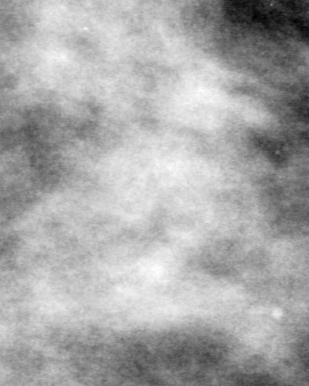
Region of interest cut from a scanned film mammogram (one marked finding), right breast, MLO view.
Marked abnormality: mass, shape architectural distortion, margins ill defined; BI-RADS assessment category 4; pathology (as recorded): benign.